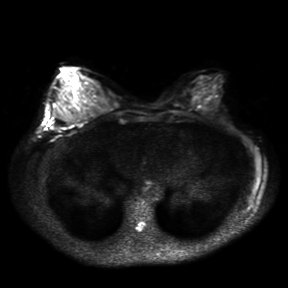
Breast MRI, one axial slice. Position 11 of 30 along the scan axis. Diffusion-weighted series; image 2 of 4 stored at this slice position (different b-values; order by instance number). 3 T. 4 mm slice thickness. 288 × 288 image matrix. Female patient.
Structures marked on this image (outlined manually by an expert reader):
- tumour on diffusion-weighted imaging: bounding box (x1, y1, x2, y2) in pixels: (53, 110, 65, 121)